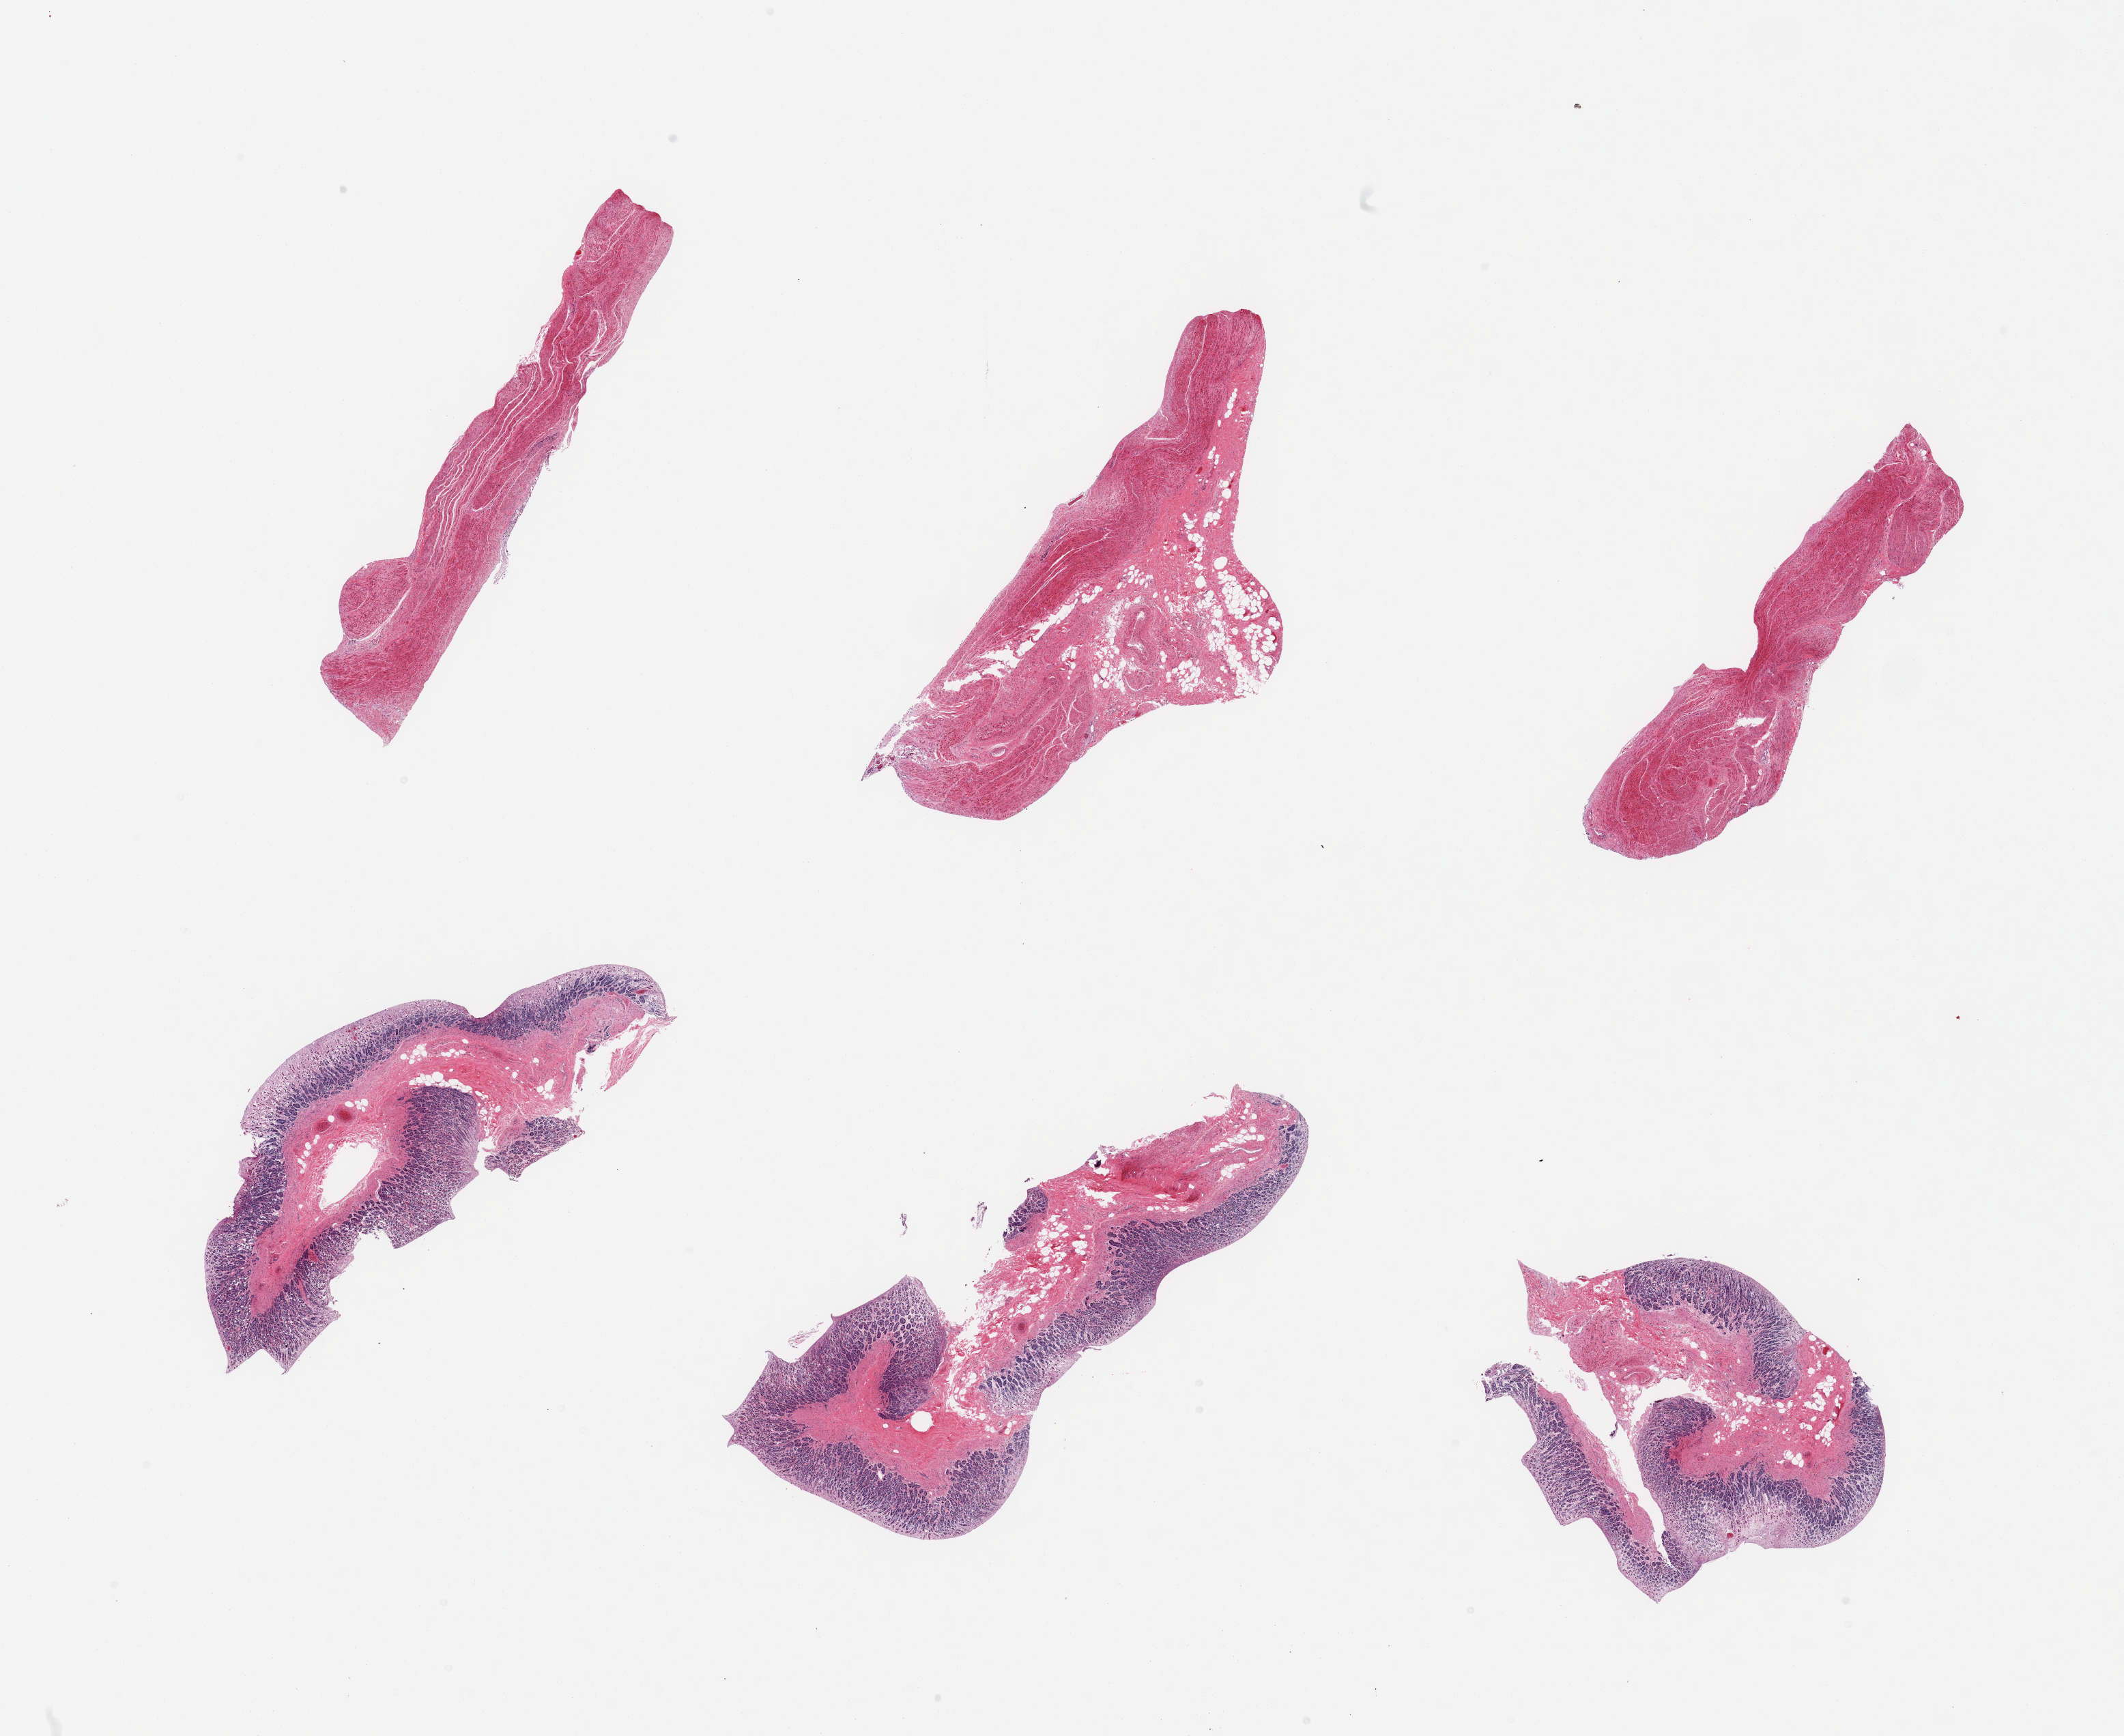
Digitized hematoxylin and eosin (H&E)-stained section — whole scanned area (about 24.6 x 20.1 mm) shown as a low-resolution overview, PAXgene-fixed paraffin-embedded (PFPE) section, section of stomach (target tissue), tissue donor sample. Donor sex: male.
Pathologist's review note for this sample: 6 pieces, mucosa up to ~0.5mm, advanced autolysis, sloughed on 3/6 pieces.